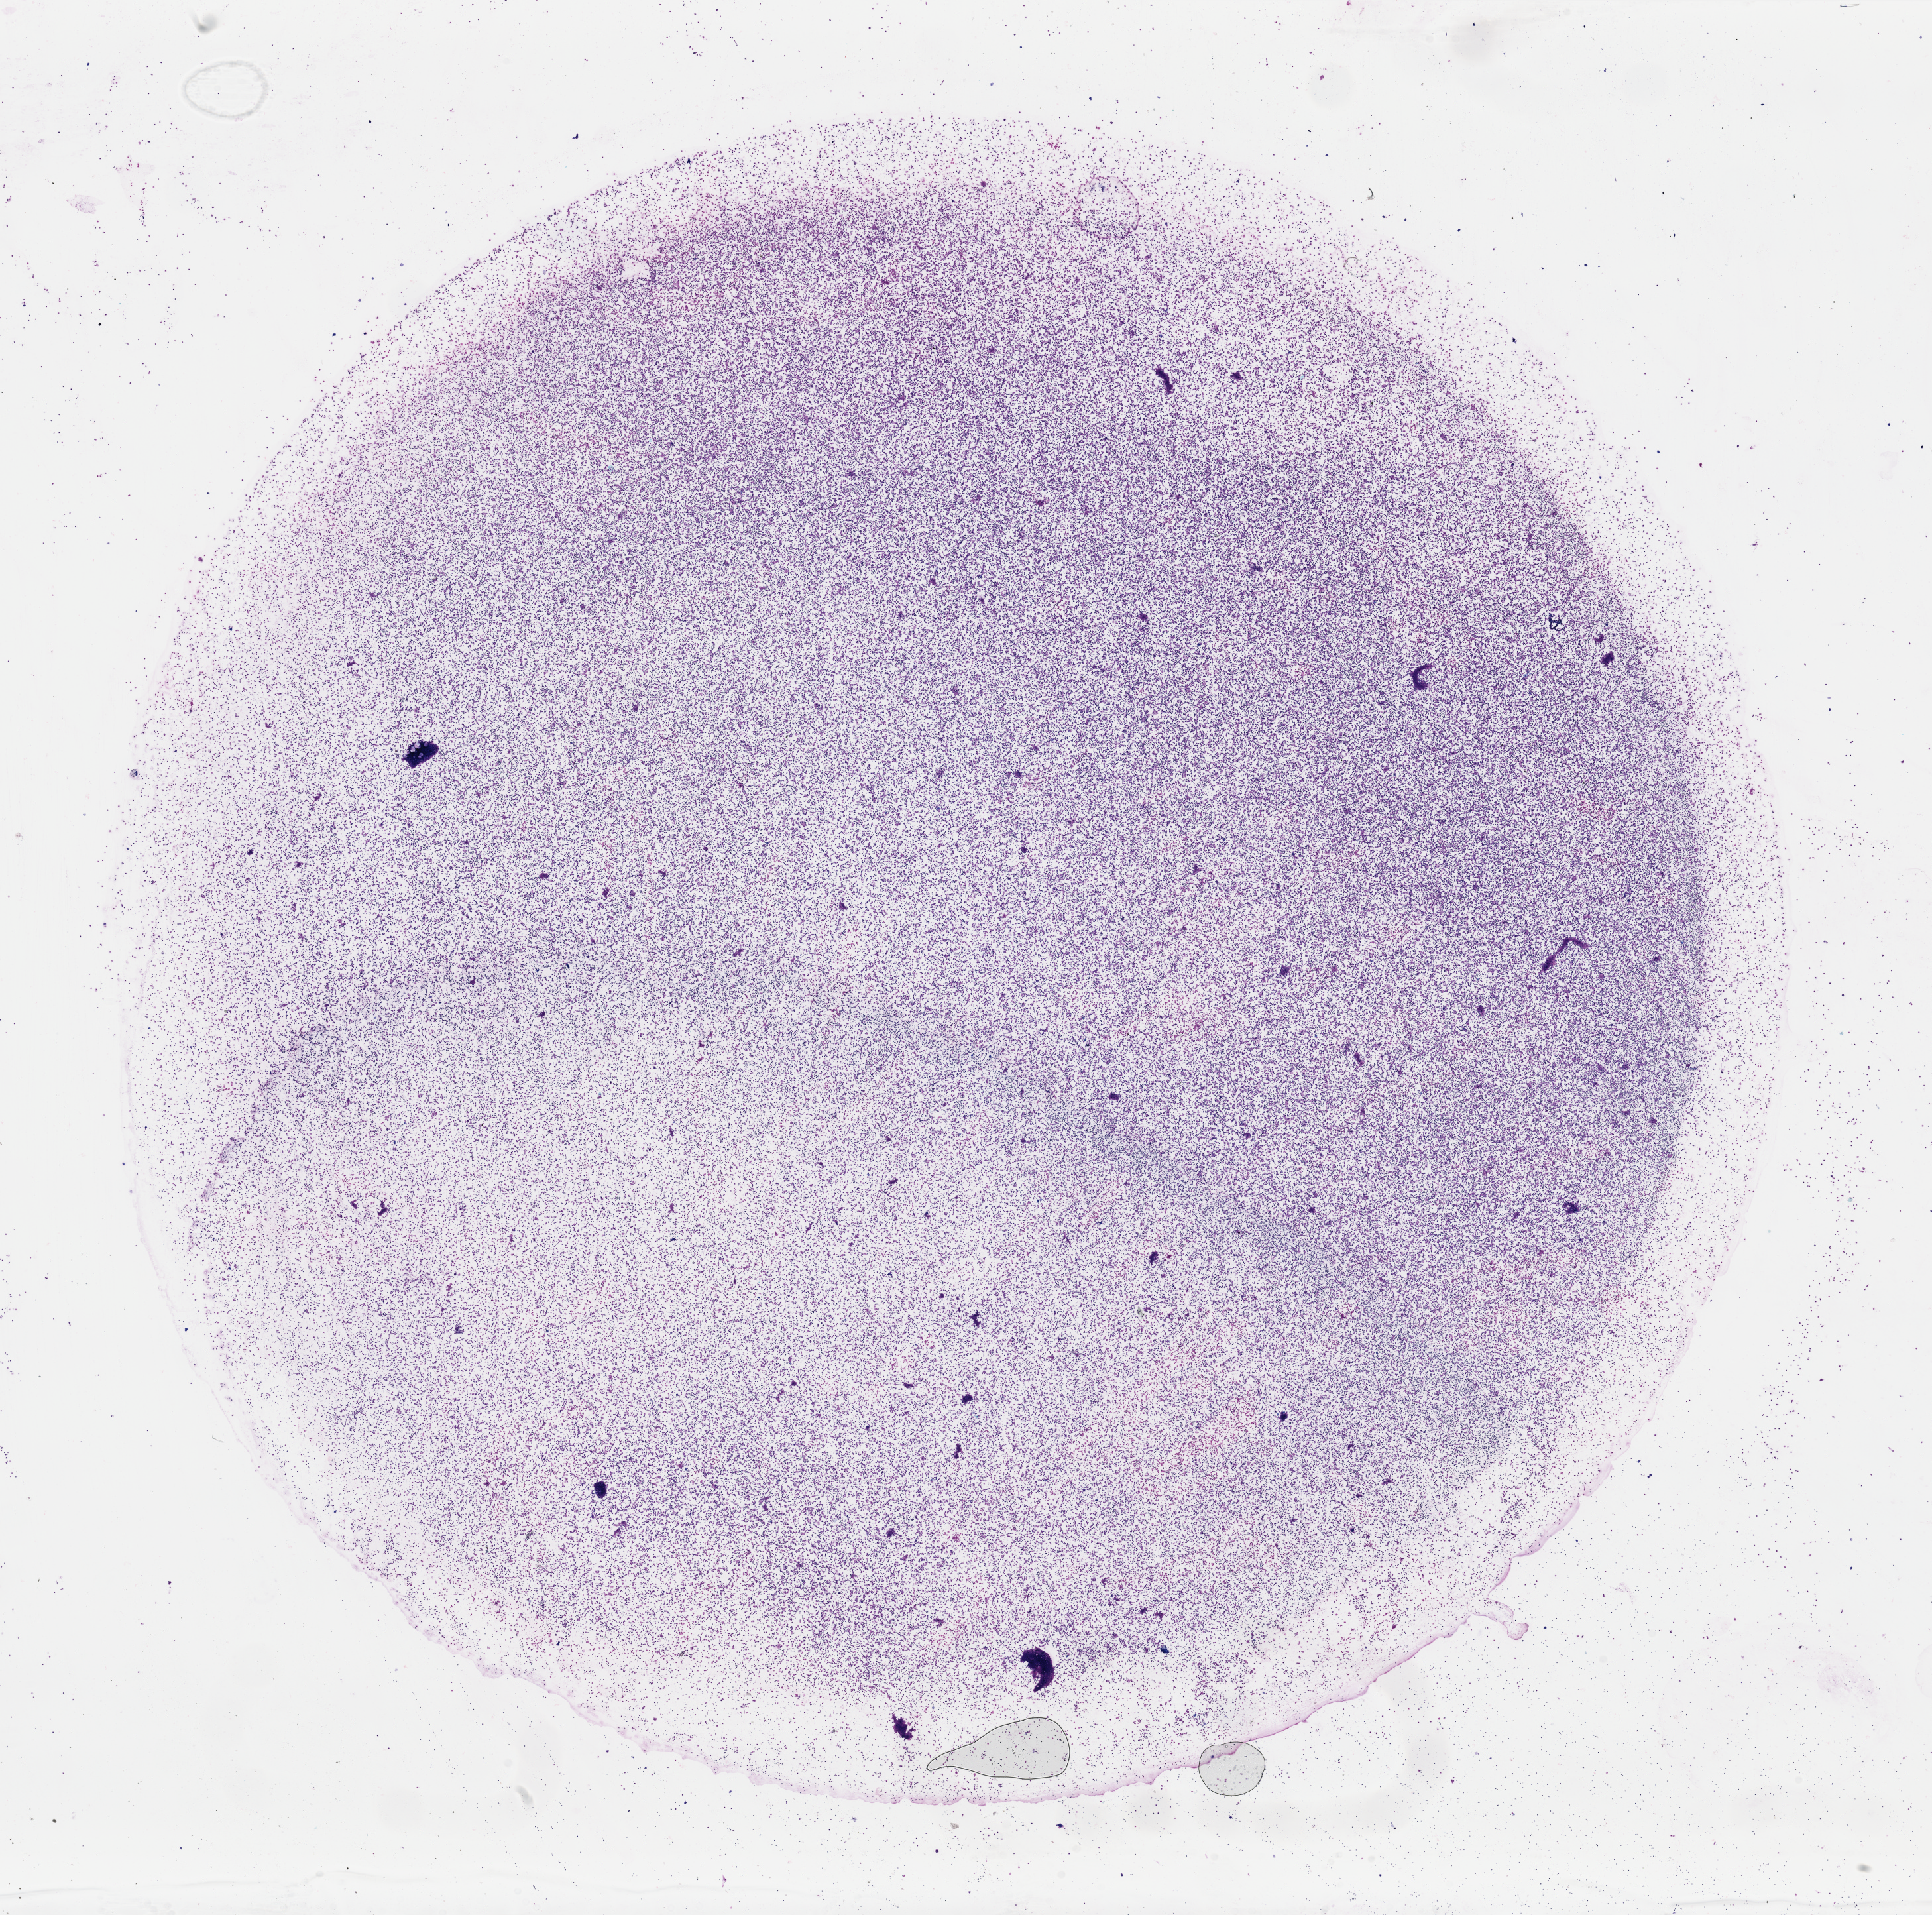
Whole-slide histology image, H&E — shown as a low-resolution overview of the whole scanned area (about 23.0 x 22.8 mm, from a 40x scan). Bone marrow (leukaemic) sample. 75-year-old male patient. Blasts: 60%.
- diagnosis: Acute Myeloid Leukemia
- FAB classification: M4
- WHO classification: Acute myelomonocytic leukemia